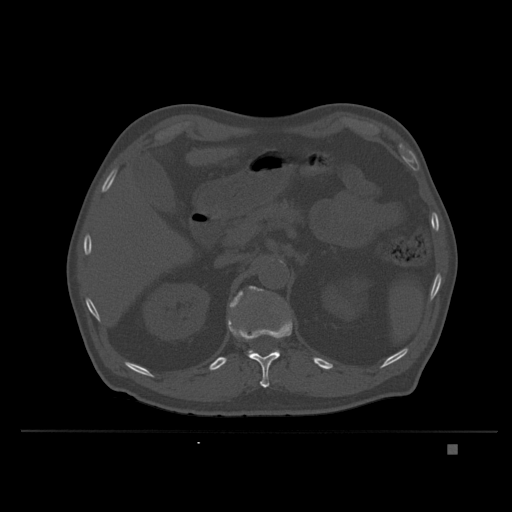
CT including the spine, one axial slice; slice 153 of 435 in the series (ordered by position); bone window (W 1800 / L 400 HU); 1.5 mm slice thickness; 512 × 512 image matrix, field of view 434 × 434 mm. Male patient, age 73 years. From the clinical record (not read from this slice): primary cancer: skin.
Structures marked on this image (semi-automatic segmentation, software-assisted and operator-edited):
- L1 vertebra: bounding box <229,287,280,358> (left, top, right, bottom; pixels)
- T12 vertebra: <228,314,293,388>